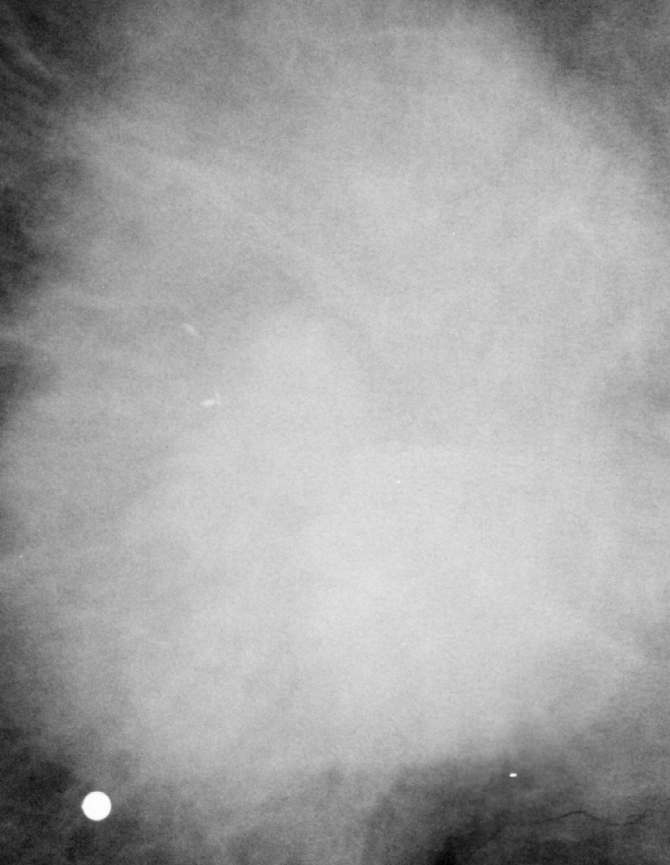
Crop from a digitized film mammogram around one marked abnormality; right breast; CC view.
Mass, shape irregular / architectural distortion, margins spiculated; BI-RADS assessment category 4; pathology (as recorded): malignant.